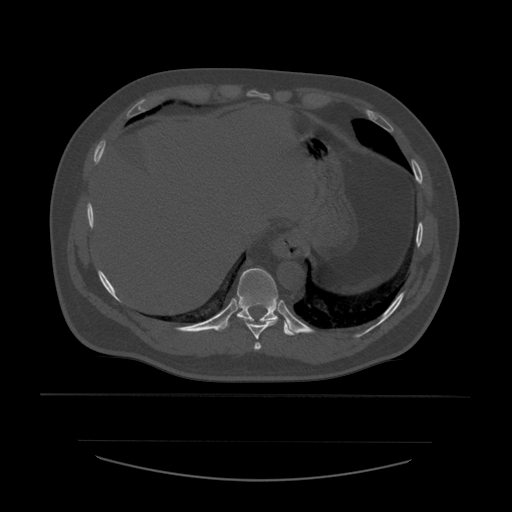
CT including the spine, one axial slice. Slice 307 of 532 in the series (ordered by position). Reconstruction kernel STANDARD. 120 kVp. Bone window (W 1800 / L 400 HU). 1.25 mm slice thickness. 512 × 512 image matrix. Patient age 44 years. Case-level facts recorded for this patient, not image findings: primary cancer: soft tissue sarcoma.
Annotated regions visible in this slice (semi-automatic segmentation, software-assisted and operator-edited):
- T10 vertebra: bounding box <217,268,299,336> (left, top, right, bottom; pixels)
- T8 vertebra: <254,342,262,350>
- T9 vertebra: <238,317,278,340>